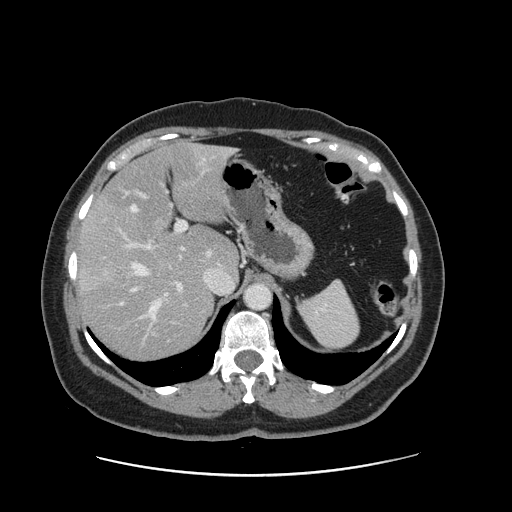
Contrast-enhanced abdominal CT, one axial slice. Position 104 of 161 along the scan axis. 120 kVp. Soft-tissue window (W 400 / L 40 HU). 2.5 mm slice thickness. 512 × 512 image matrix, field of view 398 × 398 mm. Female patient, age 62 years. From the clinical record (not read from this slice): diagnosis: colorectal cancer liver metastases, imaged before liver resection; multiple liver metastases: no; largest metastasis: 2.5 cm.
Annotated regions visible in this slice (manually delineated by an expert):
- hepatic veins: bounding box (x1, y1, x2, y2) in pixels: (131, 150, 234, 319)
- liver: (80, 144, 238, 360)
- planned liver remnant (the part of the liver to remain after resection): (102, 144, 238, 274)
- portal vein (with intrahepatic branches): (117, 170, 203, 335)
- liver metastasis: (114, 269, 129, 287)